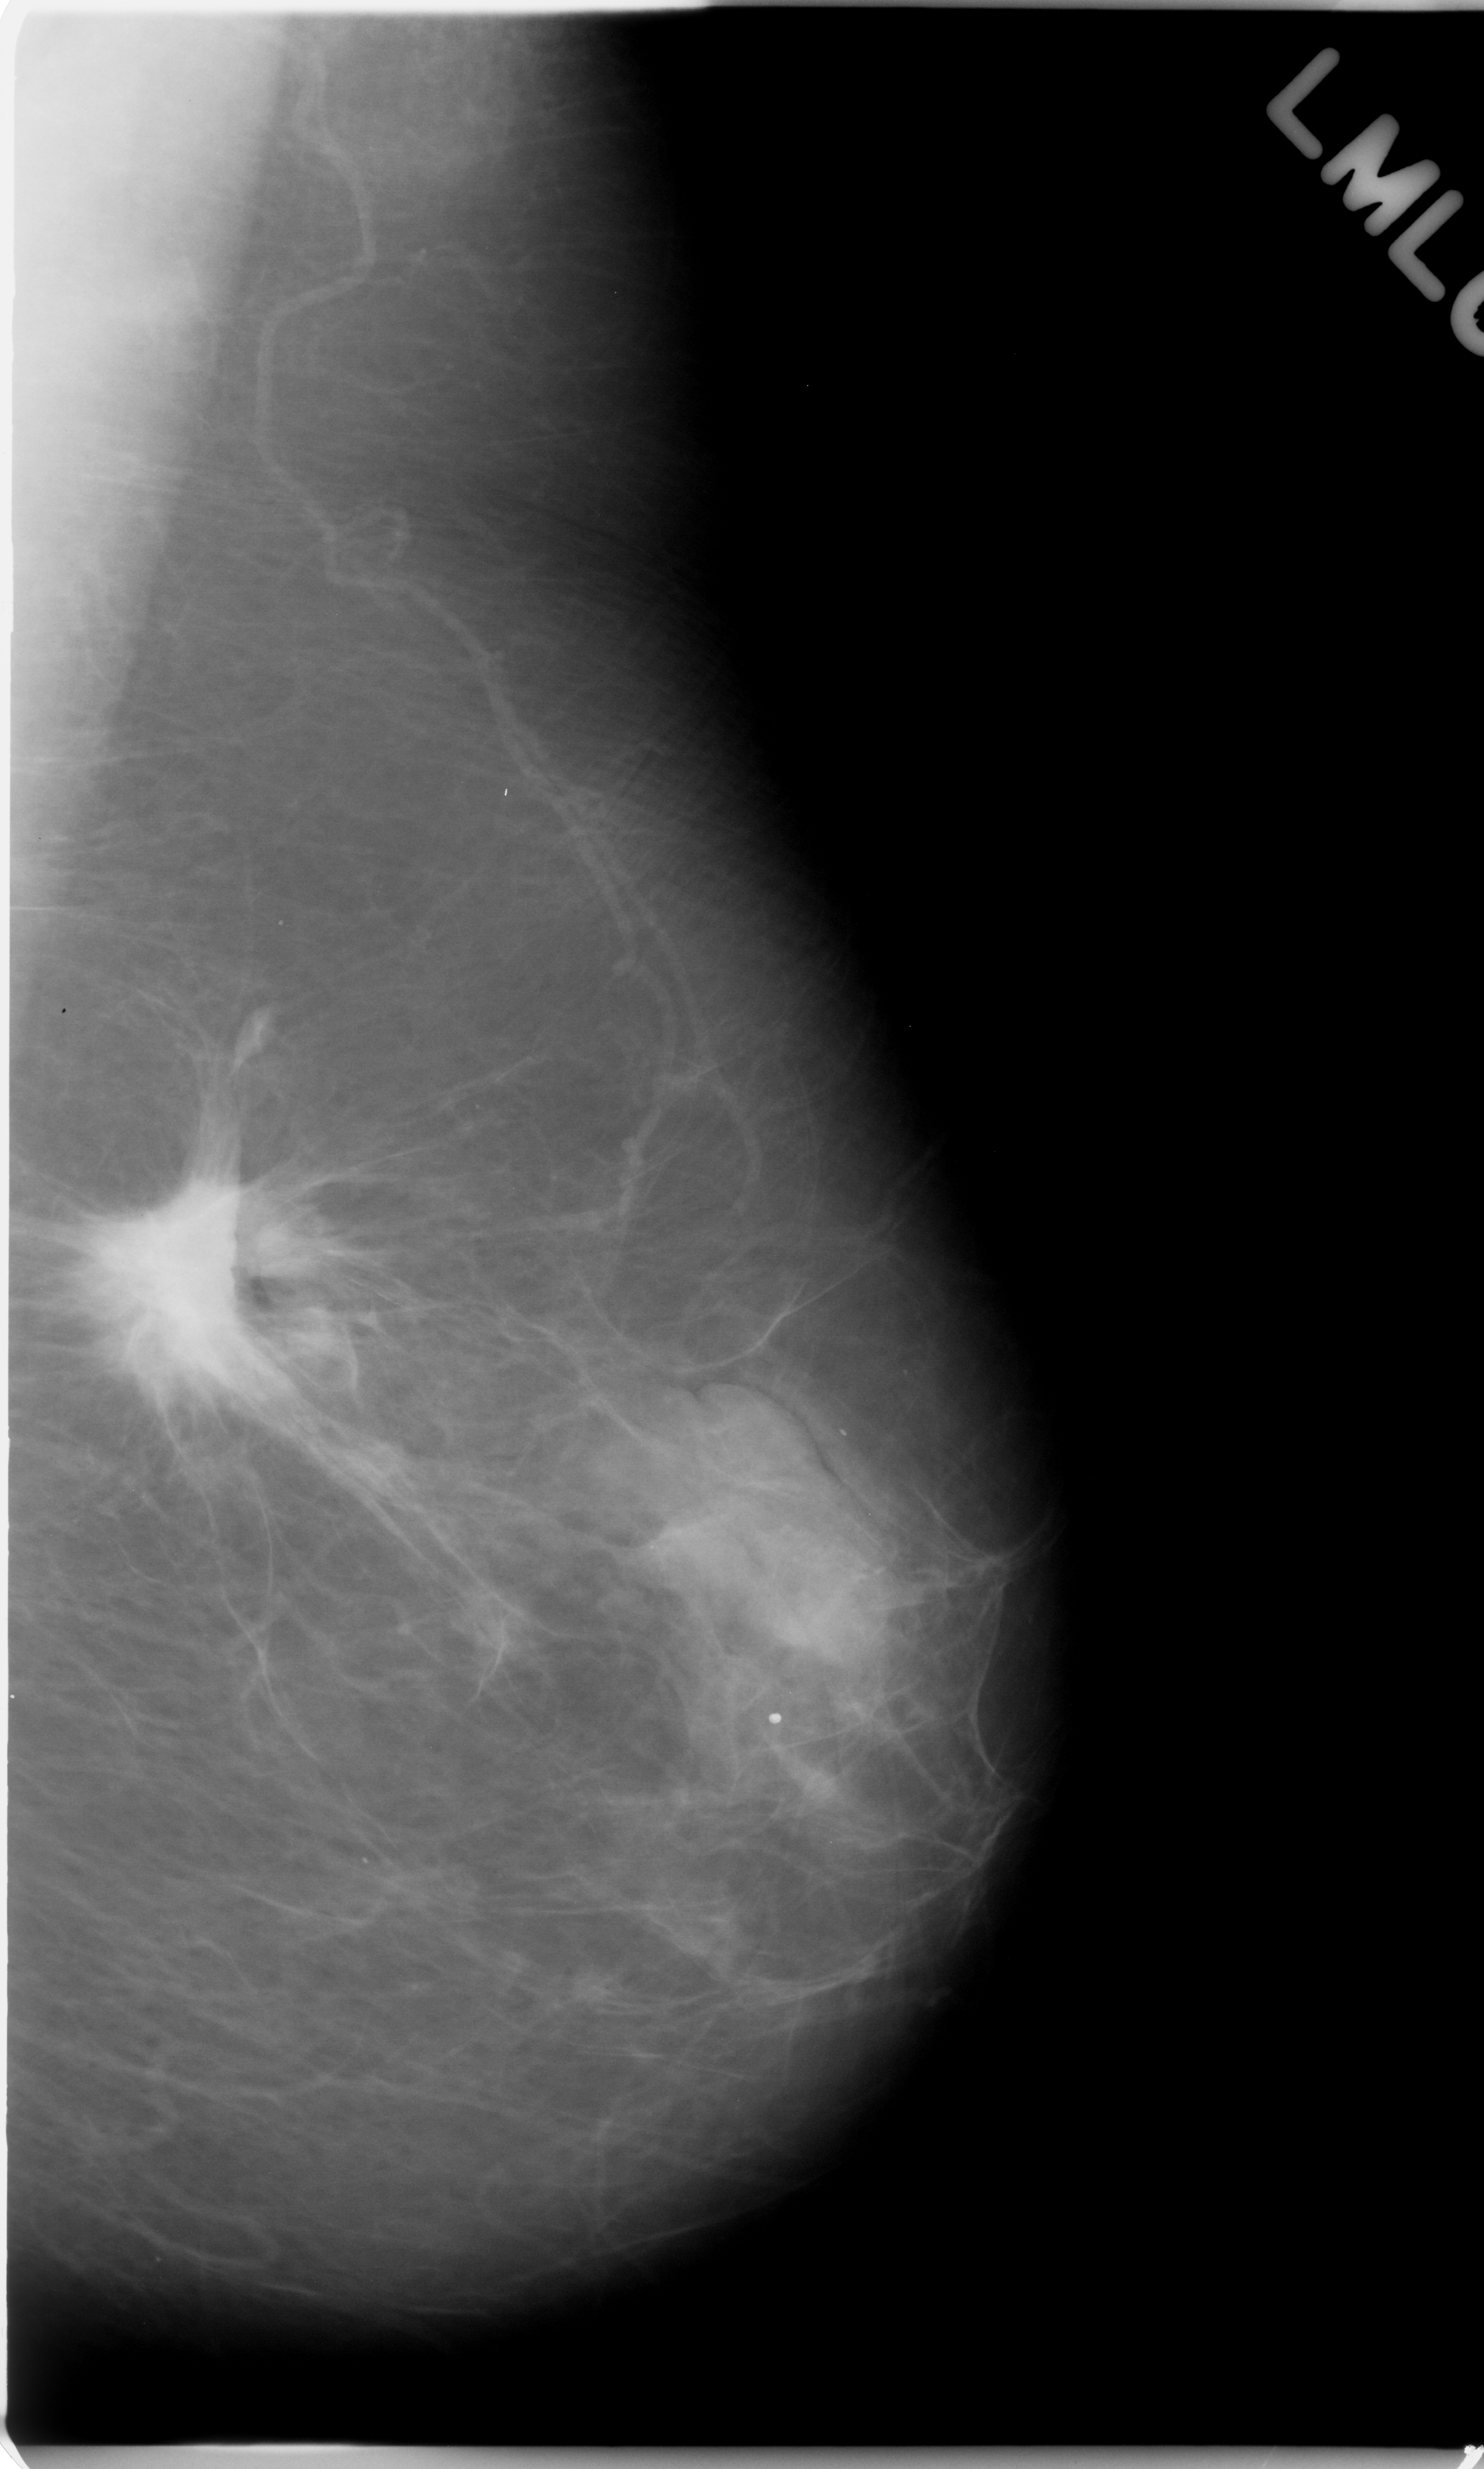
Mammogram (digitized film), left breast, mediolateral oblique (MLO) view, breast composition: almost entirely fatty (BI-RADS density category 1 of 4).
Radiologist-marked abnormalities on this image: mass, shape irregular, margins spiculated; BI-RADS assessment category 5; subtlety rating 5 on a 1 (subtle) to 5 (obvious) scale; pathology (as recorded): malignant.